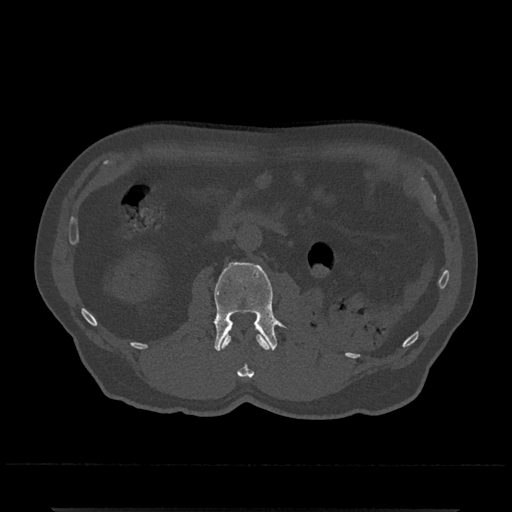
CT including the spine, one axial slice; position 308 of 797 along the scan axis; bone window (W 1800 / L 400 HU); 0.5 mm slice thickness; 512 × 512 image matrix, field of view 393 × 393 mm. Male patient, age 67 years. From the clinical record (not read from this slice): primary cancer: prostate.
Structures marked on this image (semi-automatic segmentation, software-assisted and operator-edited):
- L1 vertebra: bounding box (x1, y1, x2, y2) in pixels: (221, 334, 270, 378)
- L2 vertebra: (214, 262, 286, 351)